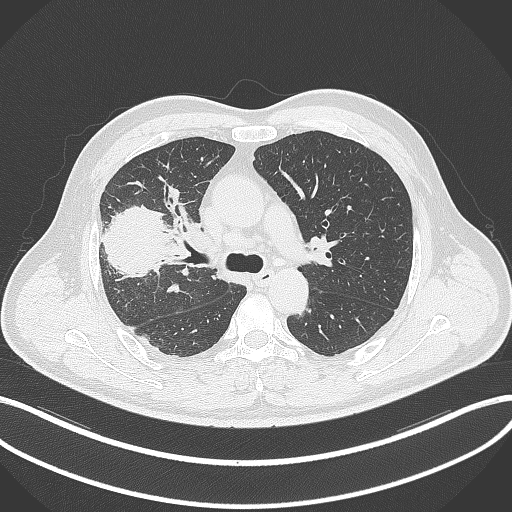
Chest CT, one axial slice; slice 217 of 348 in the series (ordered by position); 120 kVp; lung window (W 1500 / L -600 HU); 512 × 512 image matrix. Male patient, age 55 years. Case-level facts recorded for this patient, not image findings: clinical TNM (as recorded): T3 N2 M1.
Structures marked on this image (rectangle marked by the reading radiologist):
- lung tumour (recorded histology: adenocarcinoma): bounding box [x1, y1, x2, y2] px = [97, 202, 173, 279]